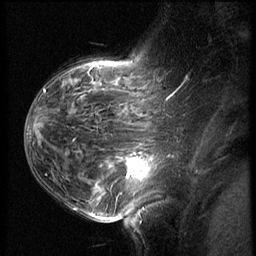
Breast MRI (dynamic contrast-enhanced), one sagittal slice. Position 41 of 62 along the scan axis. 3 images stored at this slice position (order not interpretable as contrast timing). 1.5 T. TE 4.2 ms, TR 8.9 ms. 2.5 mm slice thickness. 256 × 256 image matrix, field of view 200 × 200 mm. Patient: female, 37 years. Case-level facts recorded for this patient, not image findings: setting: breast cancer imaged before/during neoadjuvant chemotherapy; receptor status: triple-negative.
Outlined on this slice (semi-automatically segmented with operator editing):
- analysis volume of interest (the breast-tissue region the enhancement analysis was run in; not a lesion): box from (x=116, y=146) to (x=168, y=203) px
- tumour enhancement mask (voxels above the 140 % enhancement threshold inside the analysis volume of interest): (x=126, y=152)–(x=153, y=180)